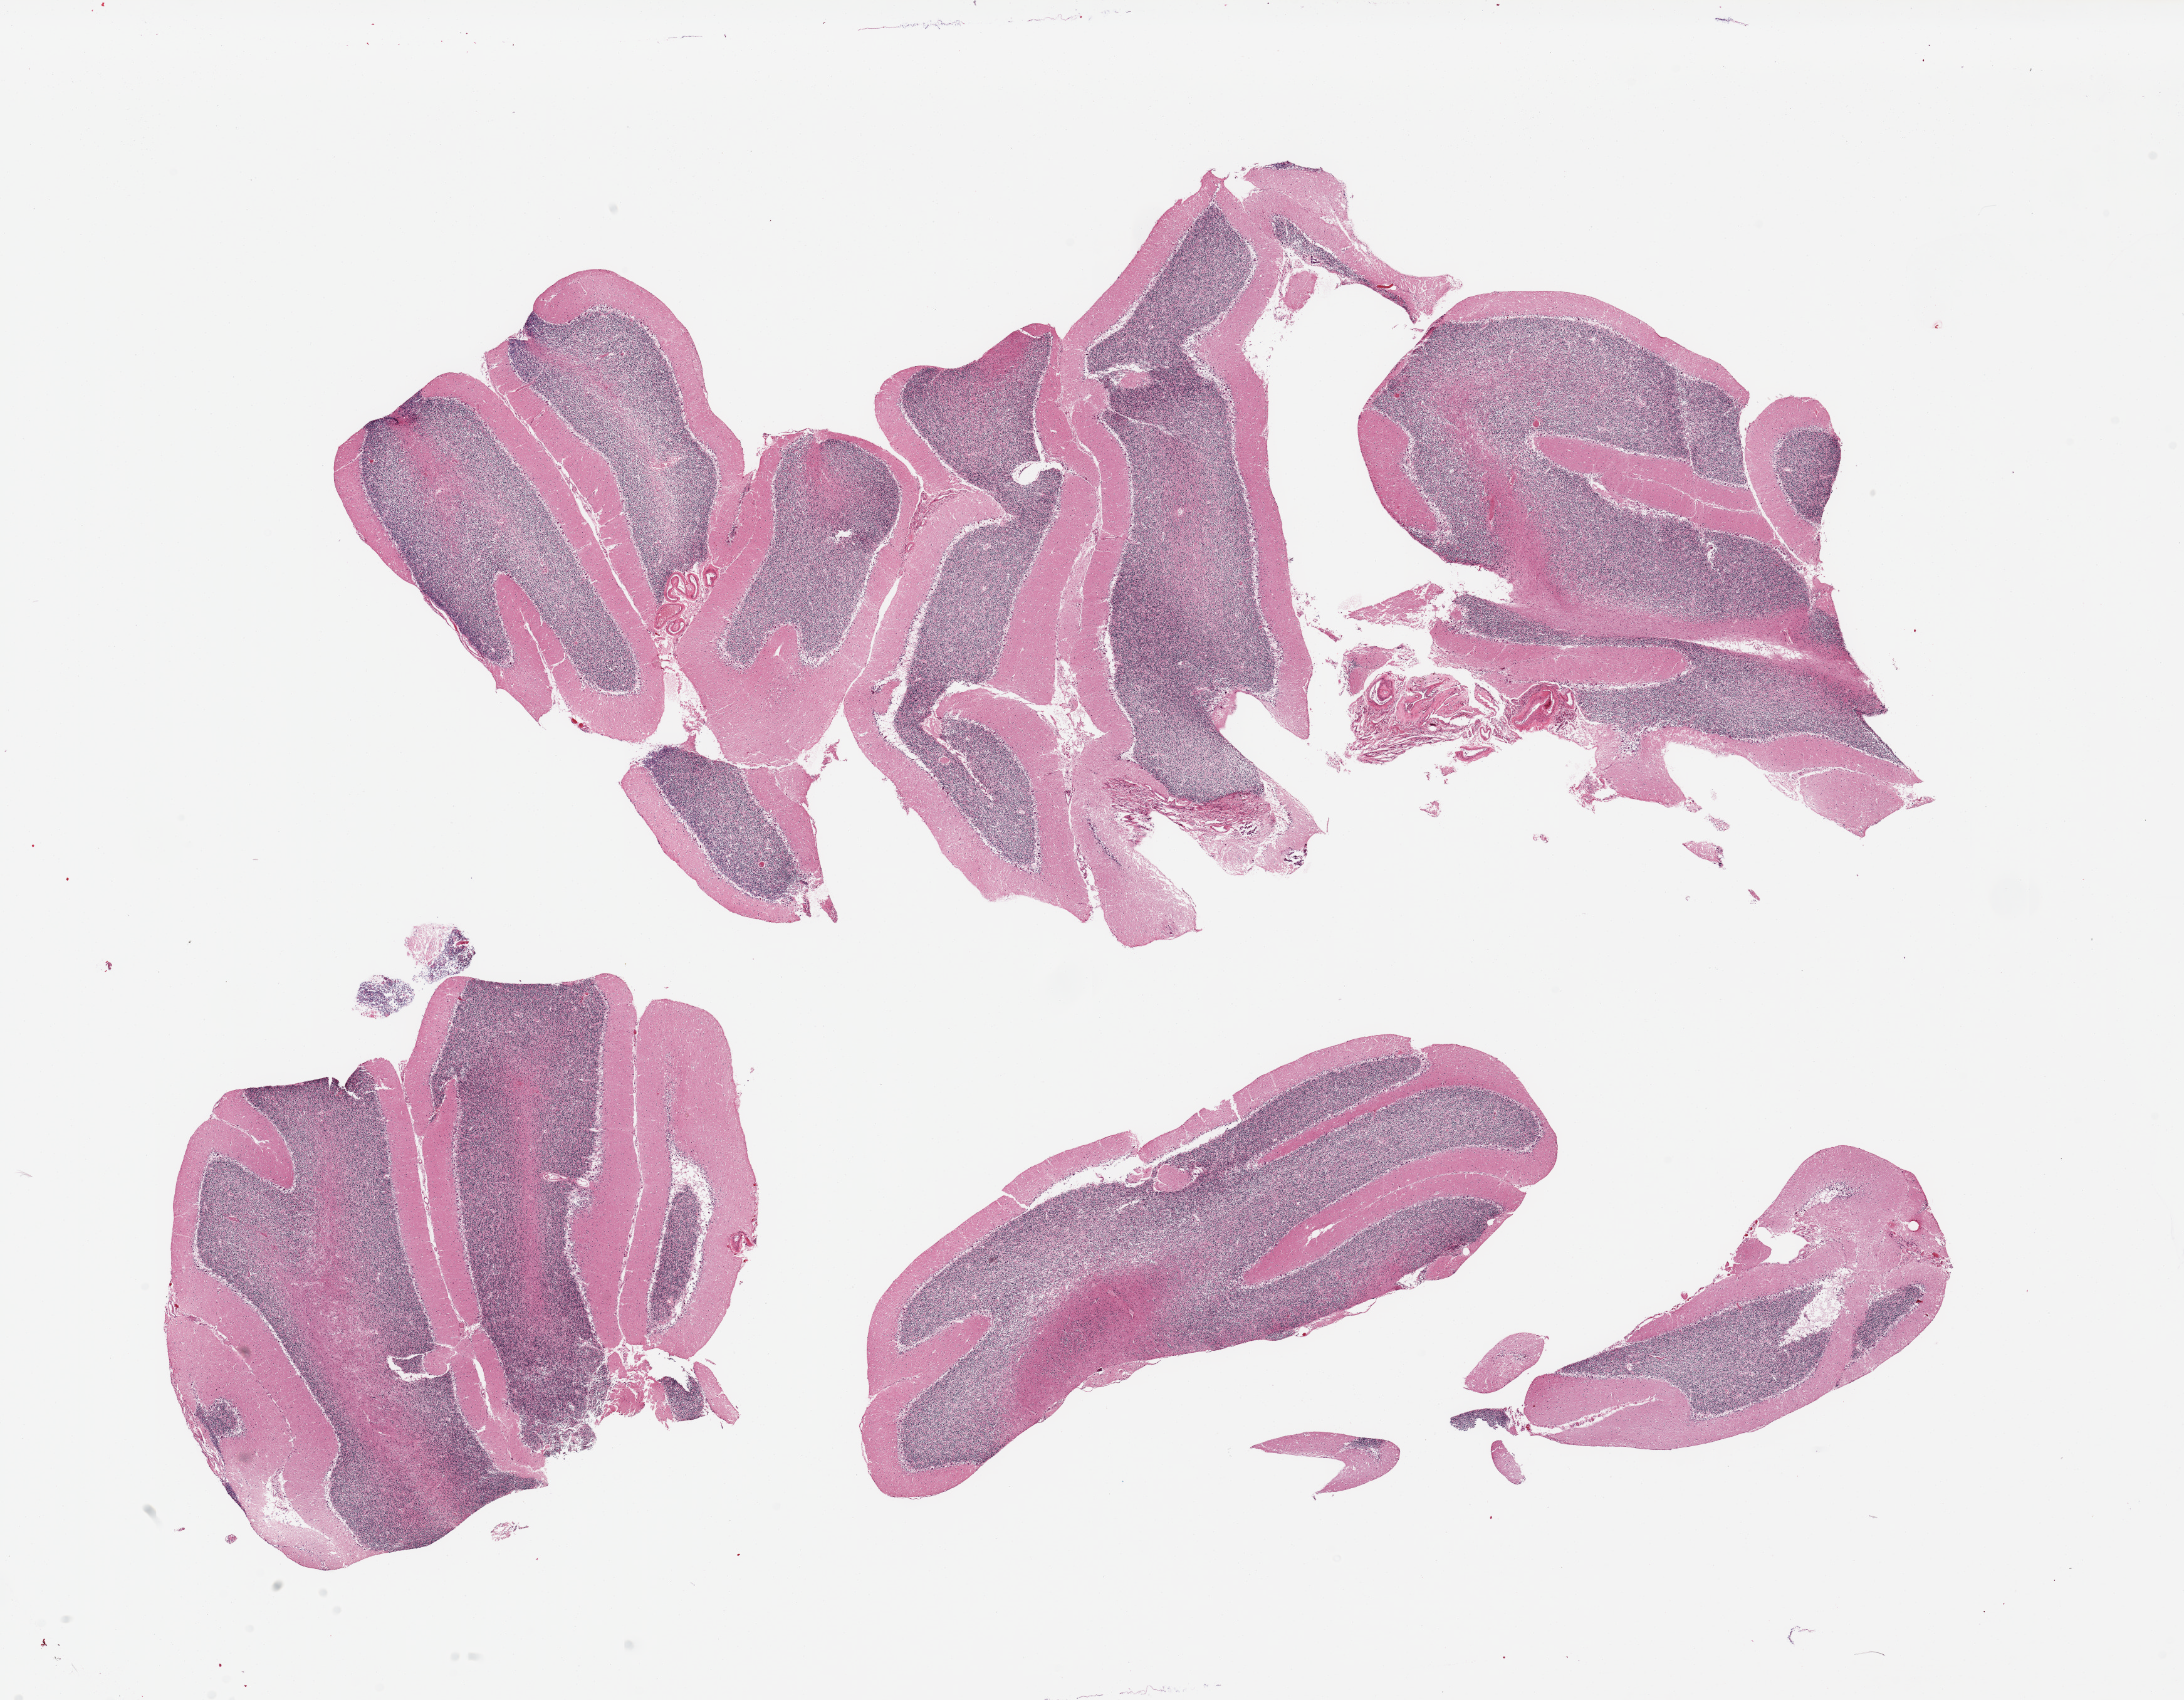
Digitized haematoxylin and eosin-stained section, a low-resolution overview of the entire scanned area, about 27.6 x 21.5 mm. PAXgene-fixed paraffin-embedded (PFPE) section. Target tissue: cerebellum. Tissue donor sample. Female donor.
- pathologist's review note for this sample: 5 pieces (fragmented) no abnormalities